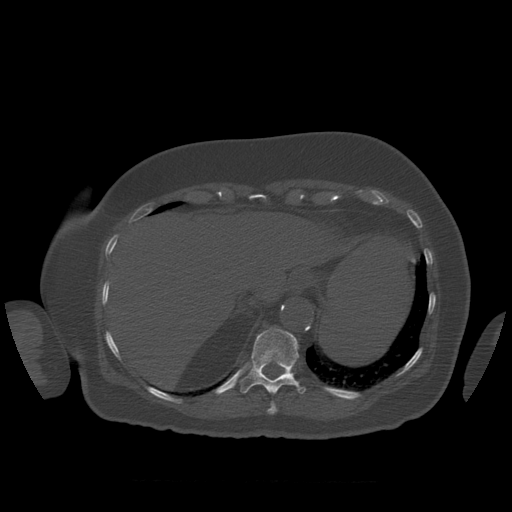
CT including the spine, one axial slice; slice 323 of 399 in the series (ordered by position); bone window (W 1800 / L 400 HU); 1.25 mm slice thickness; 512 × 512 image matrix, field of view 404 × 404 mm. Patient age 81 years. Case-level facts recorded for this patient, not image findings: primary cancer: renal.
Structures marked on this image (semi-automatically segmented with operator editing):
- T10 vertebra: bounding box <268,403,277,414> (left, top, right, bottom; pixels)
- T11 vertebra: <240,328,306,394>